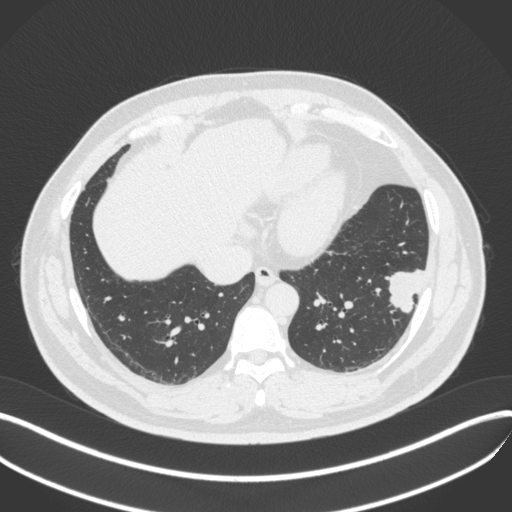
Chest CT, one axial slice. Position 132 of 420 along the scan axis. 120 kVp. Lung window (W 1500 / L -600 HU). 512 × 512 image matrix, field of view 400 × 400 mm. Male patient, age 39 years. From the clinical record (not read from this slice): clinical TNM (as recorded): T2a N0 M0; histopathological grade: G2-3.
Outlined on this slice (rectangle marked by the reading radiologist):
- lung tumour (recorded histology: adenocarcinoma): bounding box [x1, y1, x2, y2] px = [382, 263, 428, 316]